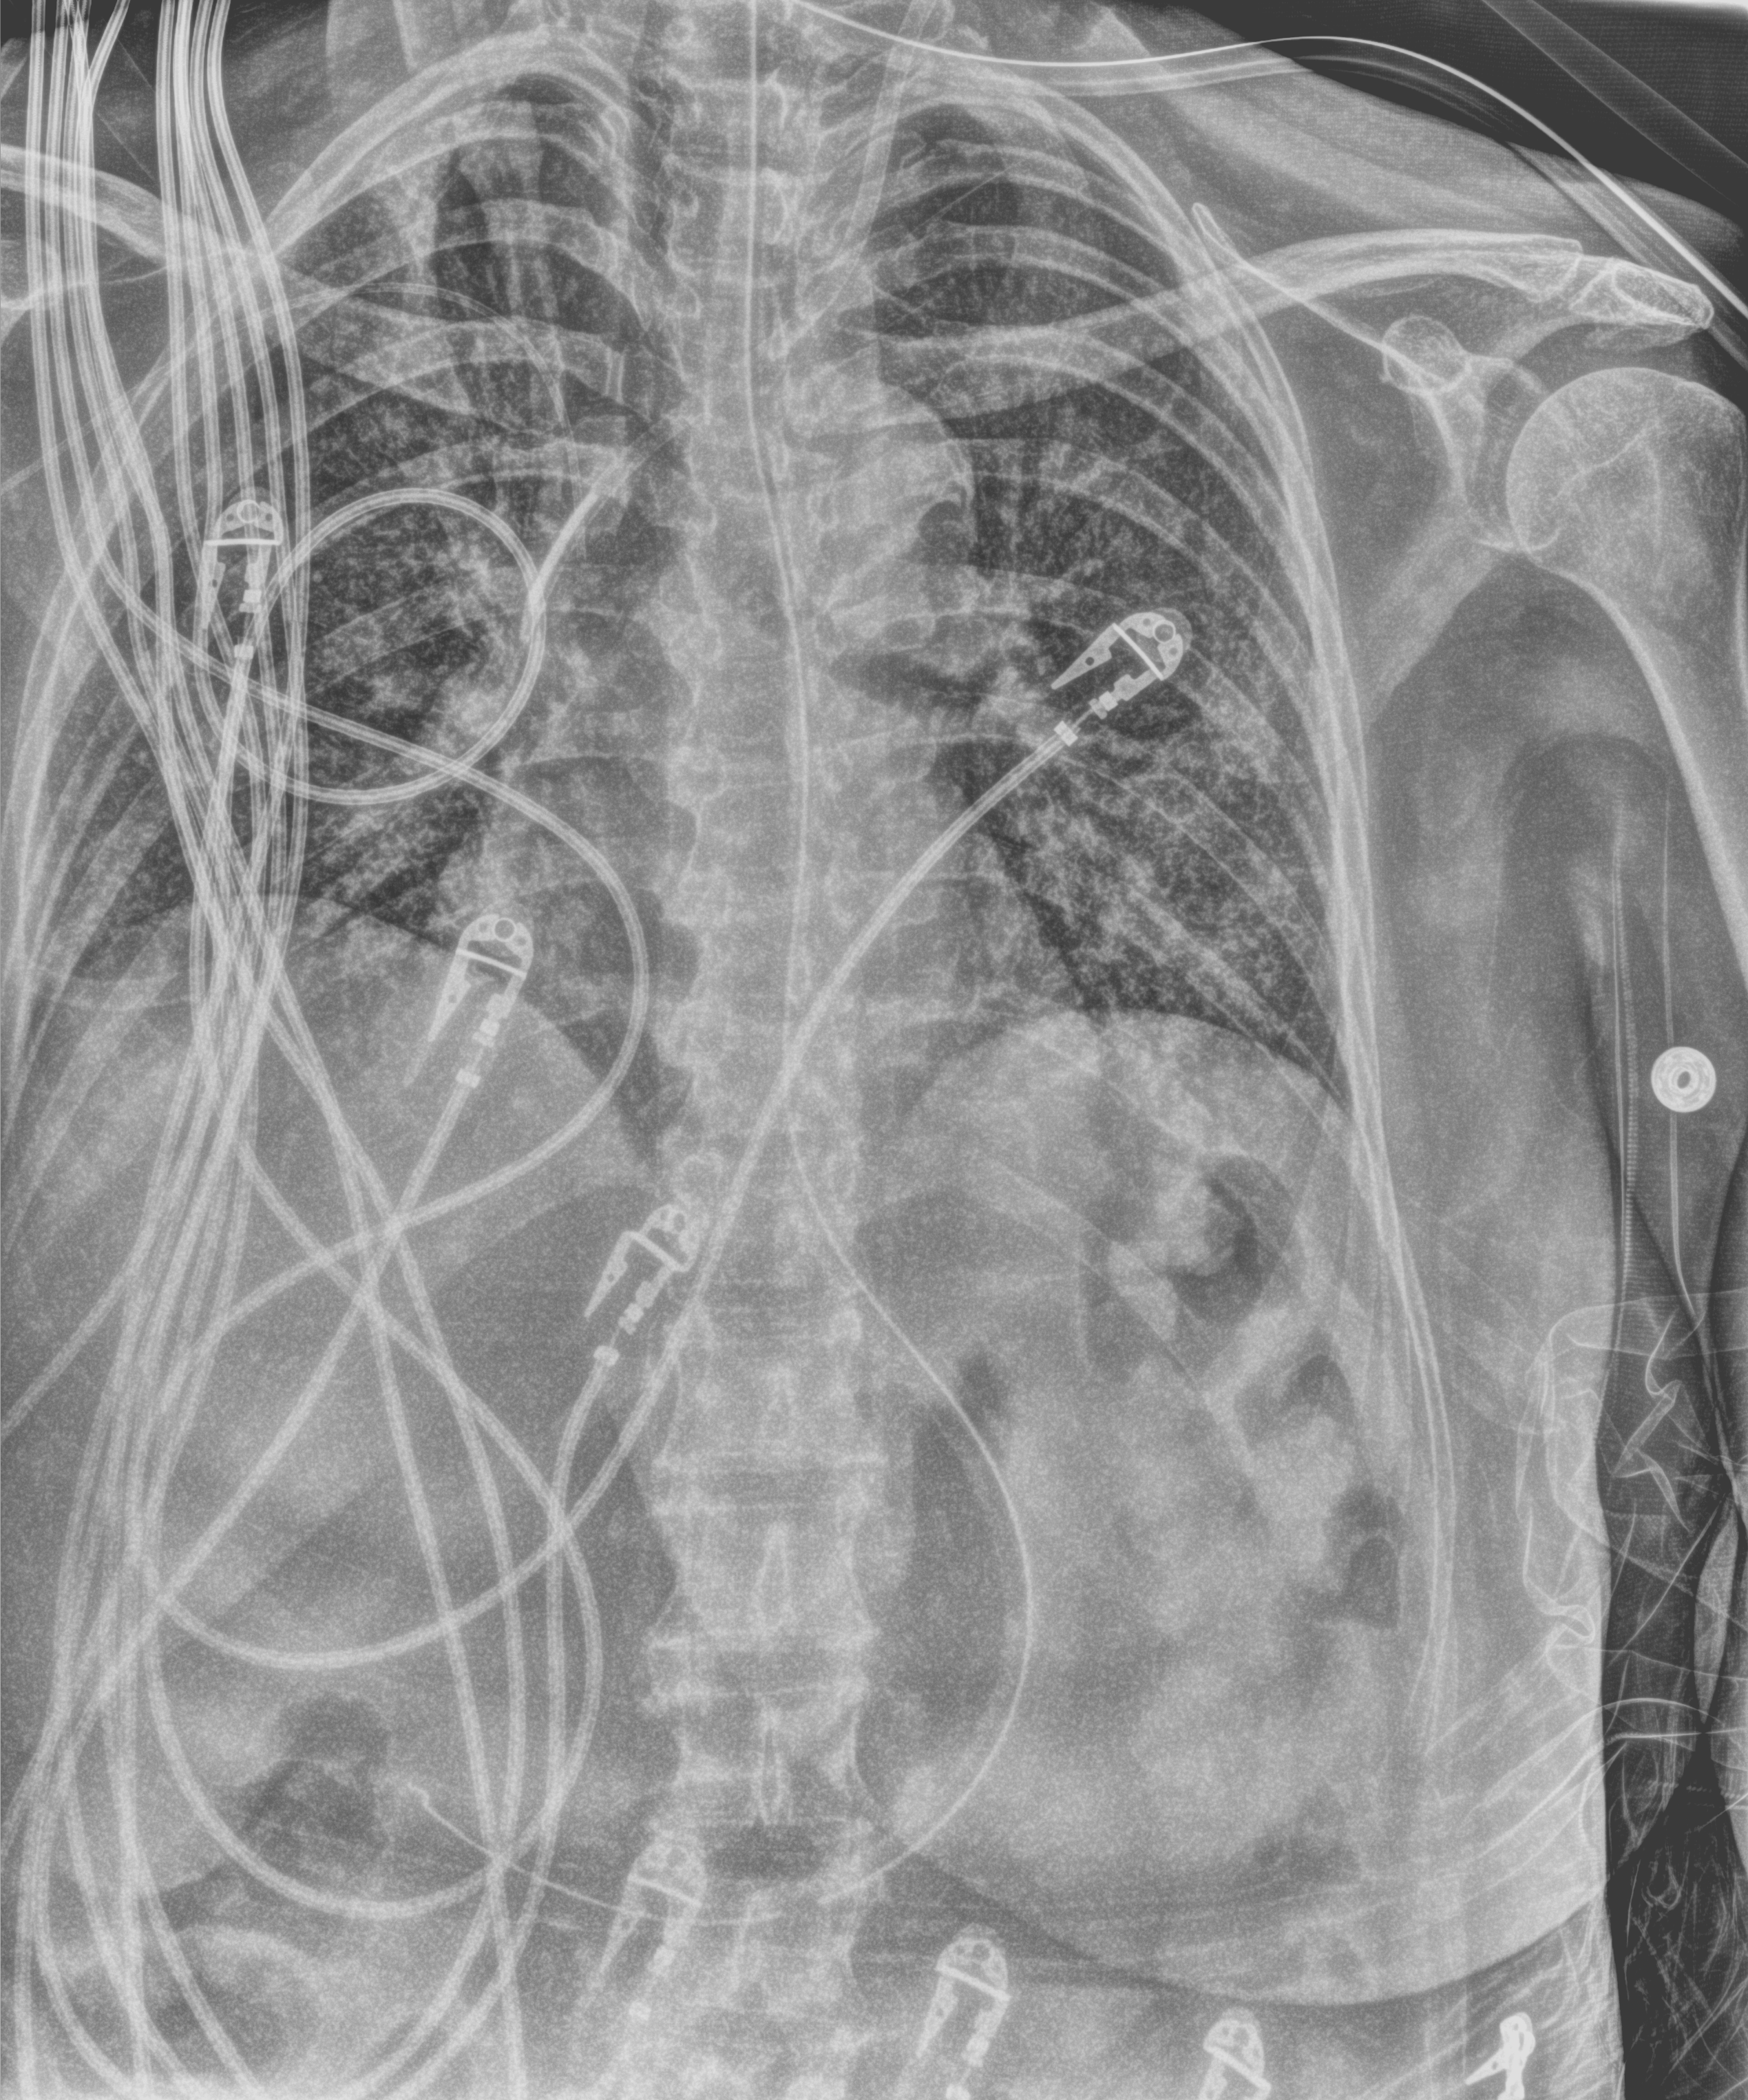
Chest X-ray (portable), anteroposterior (AP) projection. Female patient hospitalised with COVID-19, age 60–74 years.
From the hospital-stay record, not from the radiograph (when in the stay this image was taken is not recorded):
- diabetes (admission record): no
- admitted to intensive care during this hospital stay: yes
- mechanically ventilated during this hospital stay: yes